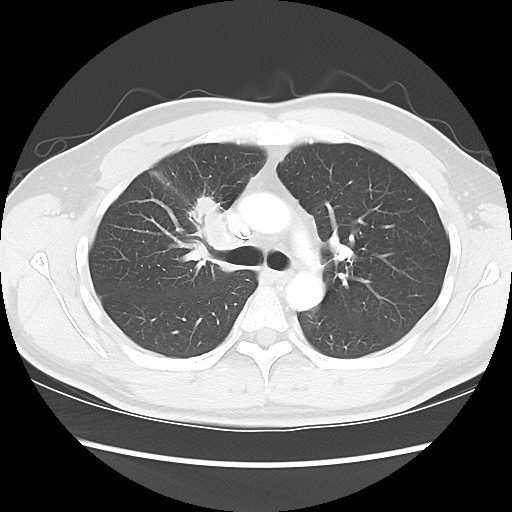
Chest CT, one axial slice; slice 61 of 80 in the series (ordered by position); reconstruction kernel LUNG; 120 kVp; lung window (W 1500 / L -600 HU); 512 × 512 image matrix. Male patient, age 35 years. Case-level facts recorded for this patient, not image findings: clinical TNM (as recorded): T1c N1 M1b.
Annotated regions visible in this slice (bounding box drawn by a radiologist):
- lung tumour (recorded histology: adenocarcinoma): bounding box <189,192,238,256> (left, top, right, bottom; pixels)